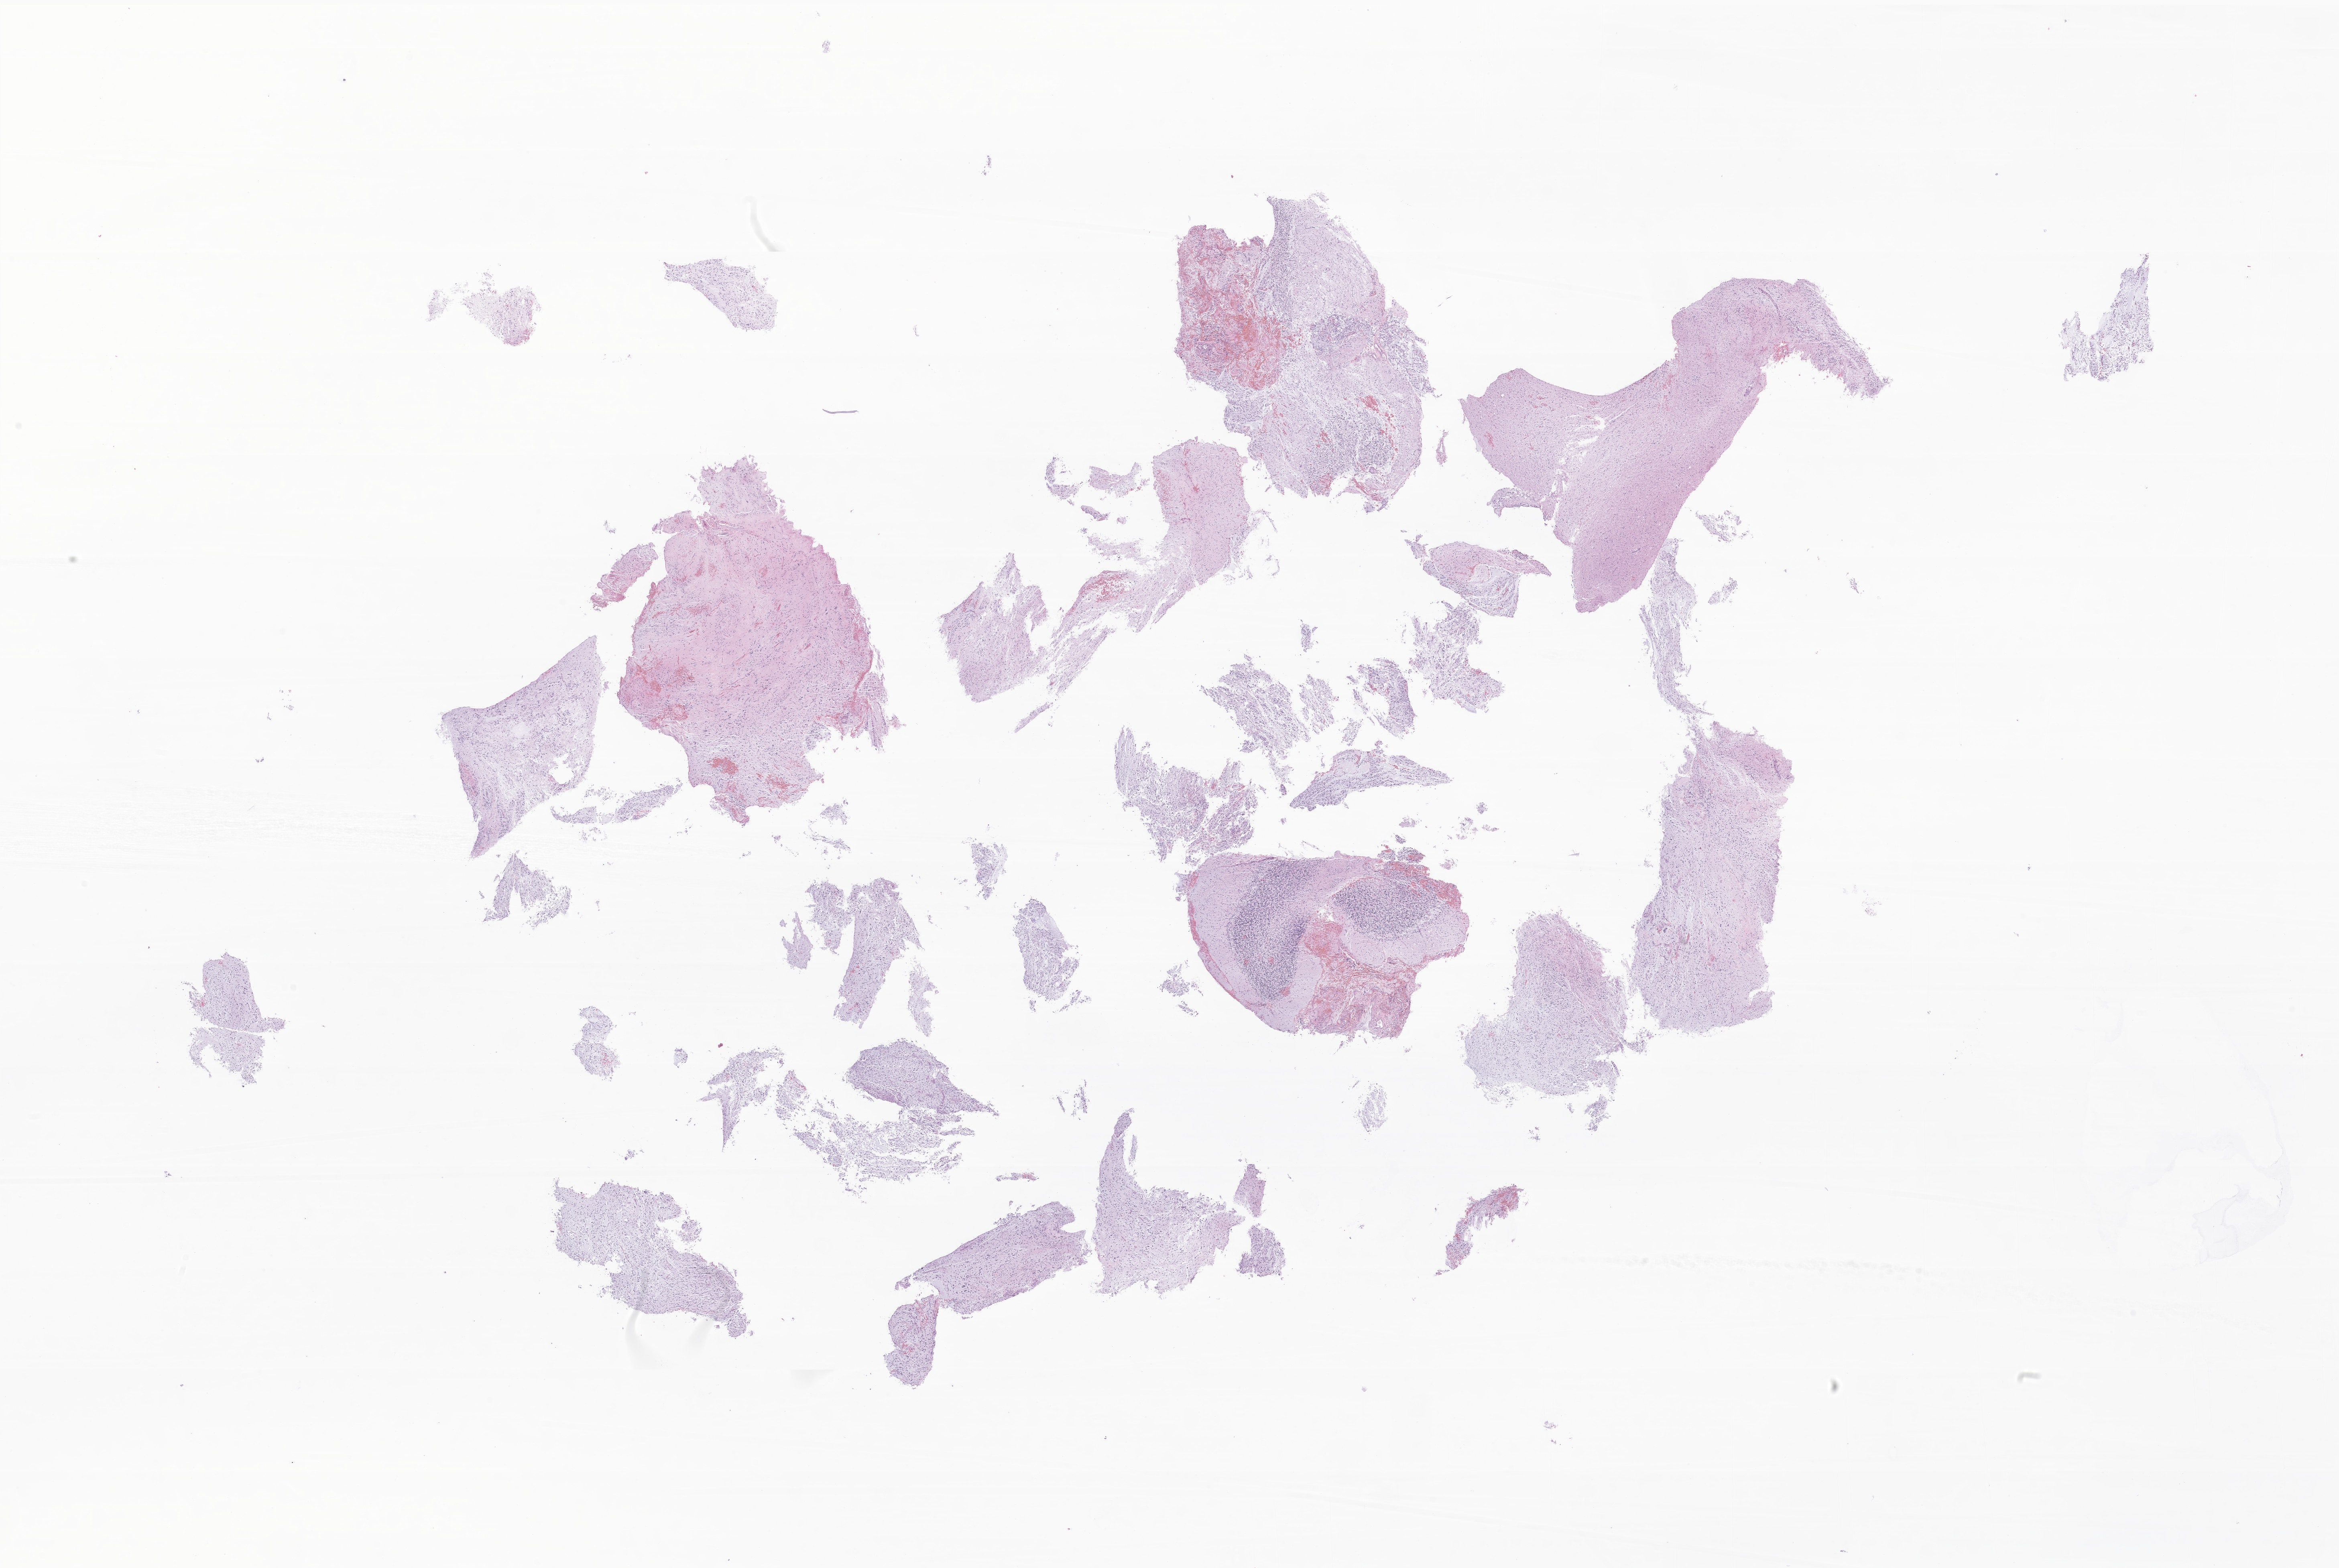
Digitized hematoxylin and eosin (H&E)-stained section of tumor tissue from the brain — a low-resolution overview of the entire scanned area, about 24.6 x 16.5 mm; formalin-fixed, paraffin-embedded (FFPE) tissue. Patient: female, age 202 months (16 years 10 months).
Diagnosis: Neoplasm, benign.